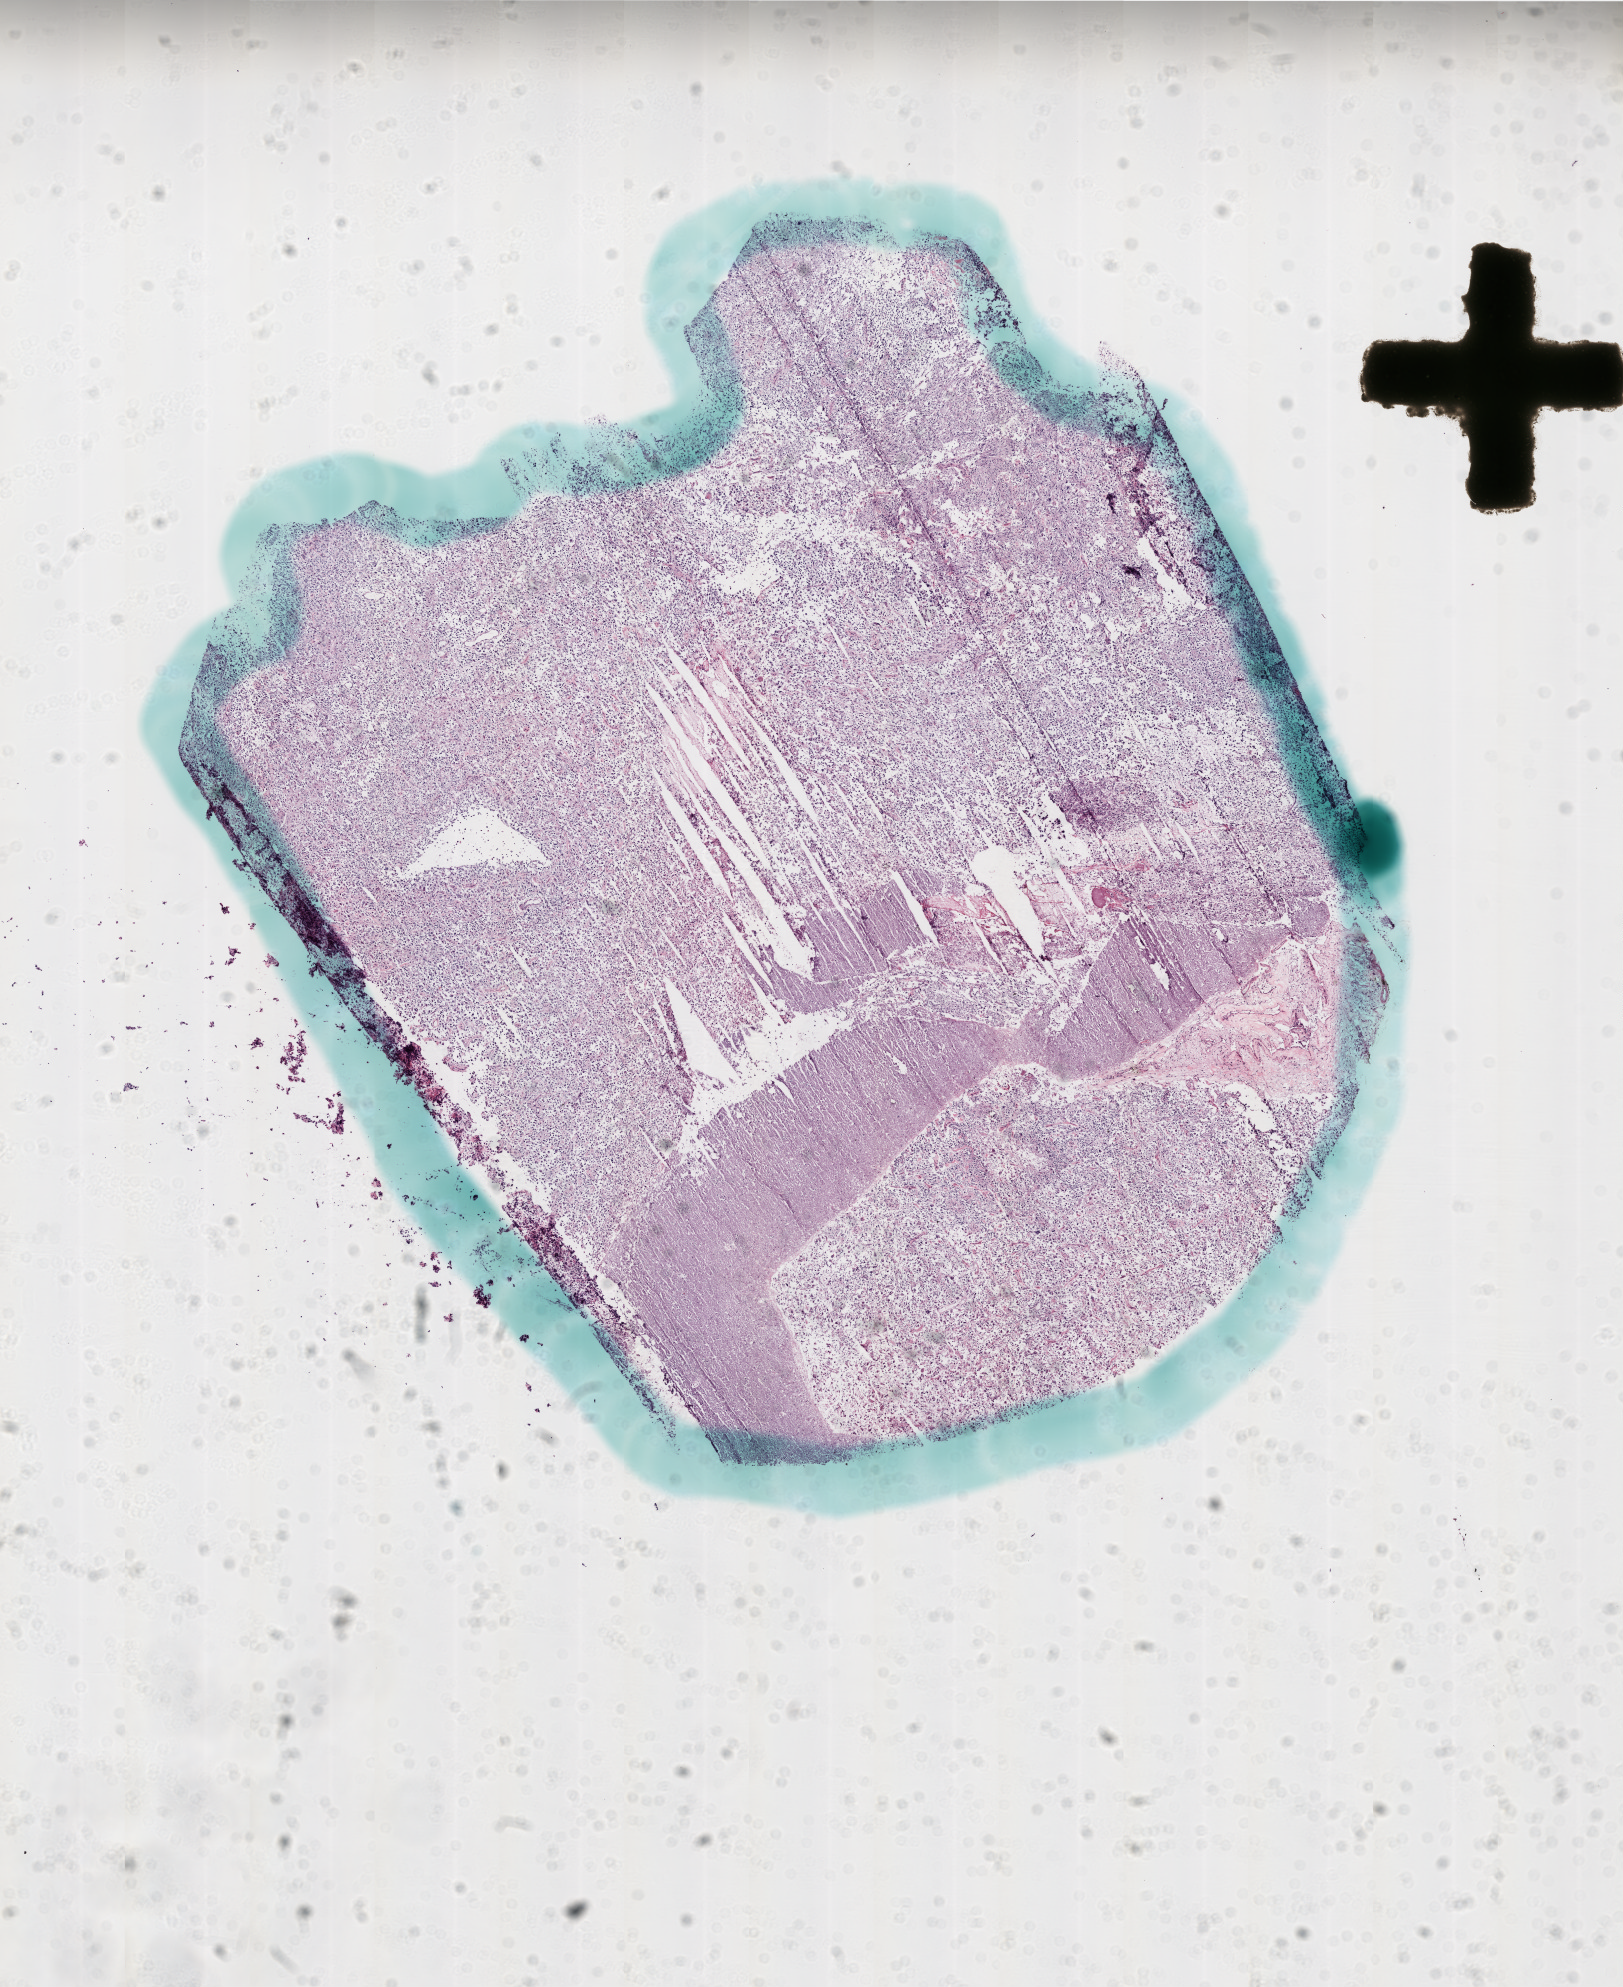
H&E-stained whole-slide image, shown as a low-resolution overview of the whole scanned area (about 13.0 x 15.9 mm, from a 20x scan). Frozen section. Brain, primary tumour sample. Patient: male, age at initial diagnosis 63 years. Pathologist review of this section (percent, as recorded): tumour cells 80%, tumour nuclei 95%, normal cells 15%, stromal cells 0%, necrosis 5%.
• pathologic diagnosis: Glioblastoma